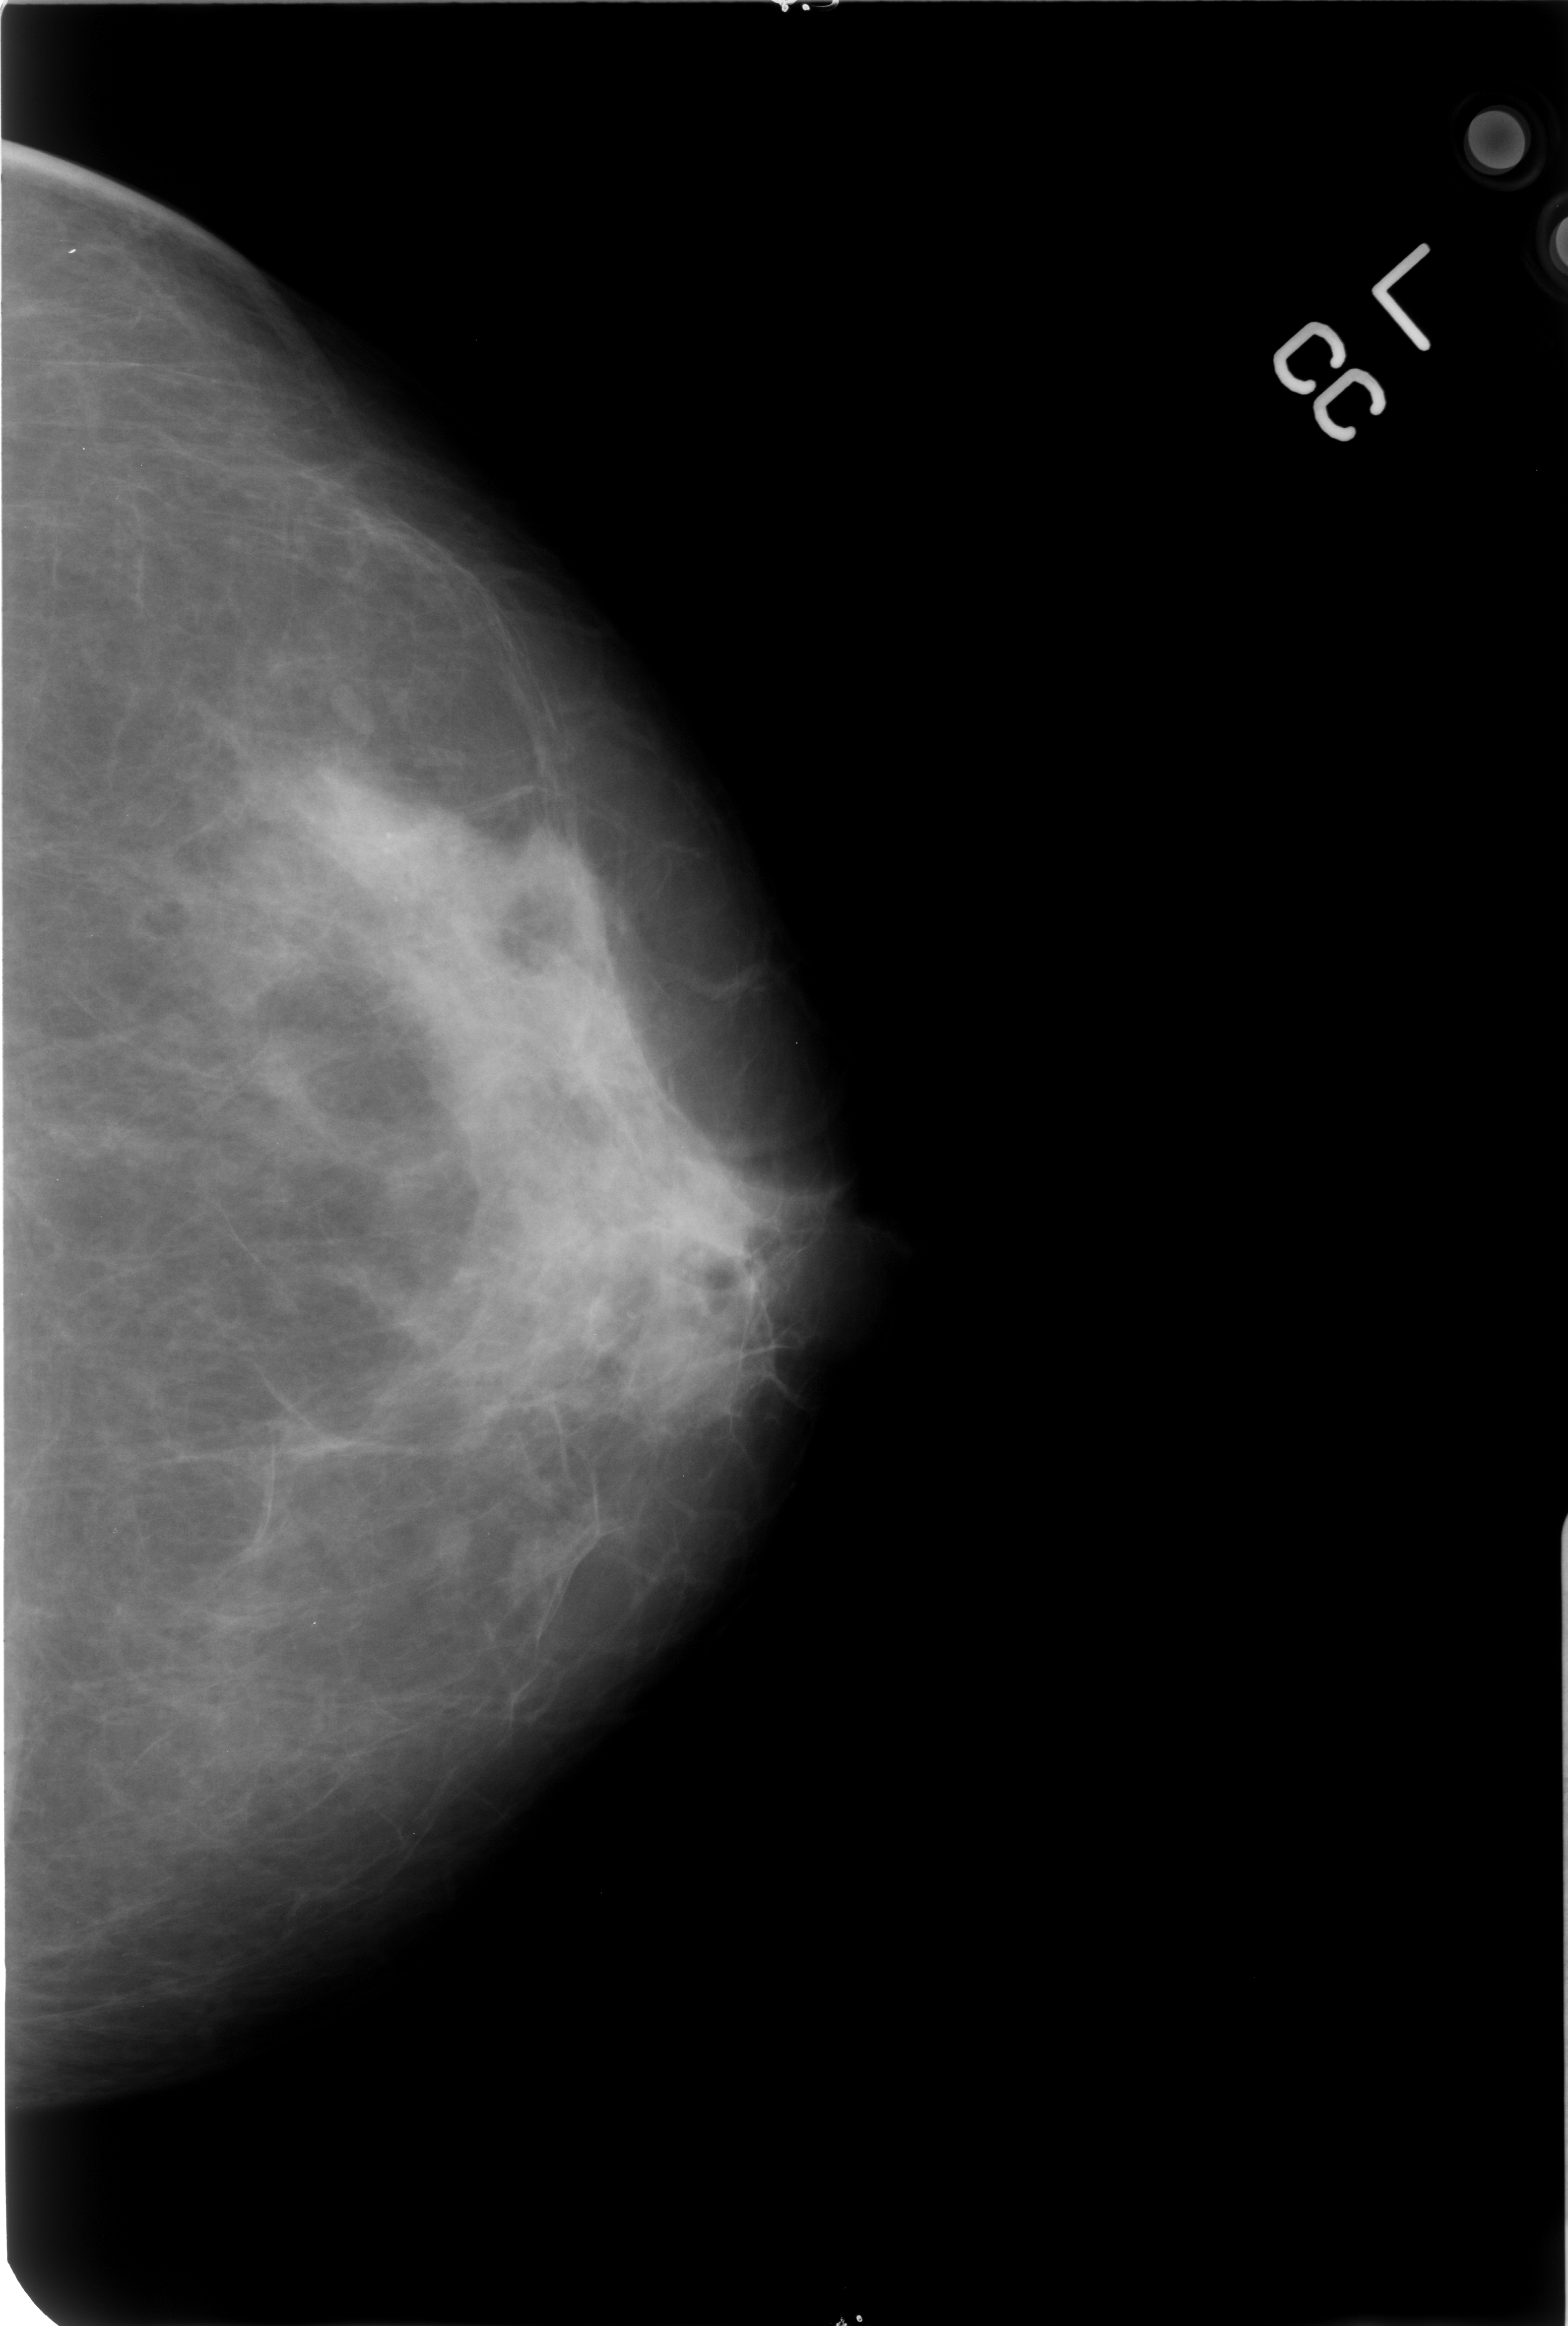
Digitized screen-film mammogram, left breast, craniocaudal (CC) view, BI-RADS breast density category 3 (scale 1–4).
Abnormality record for this image: calcifications, morphology punctate, distribution clustered; BI-RADS assessment category 2; benign; no additional work-up was recommended (benign without callback).